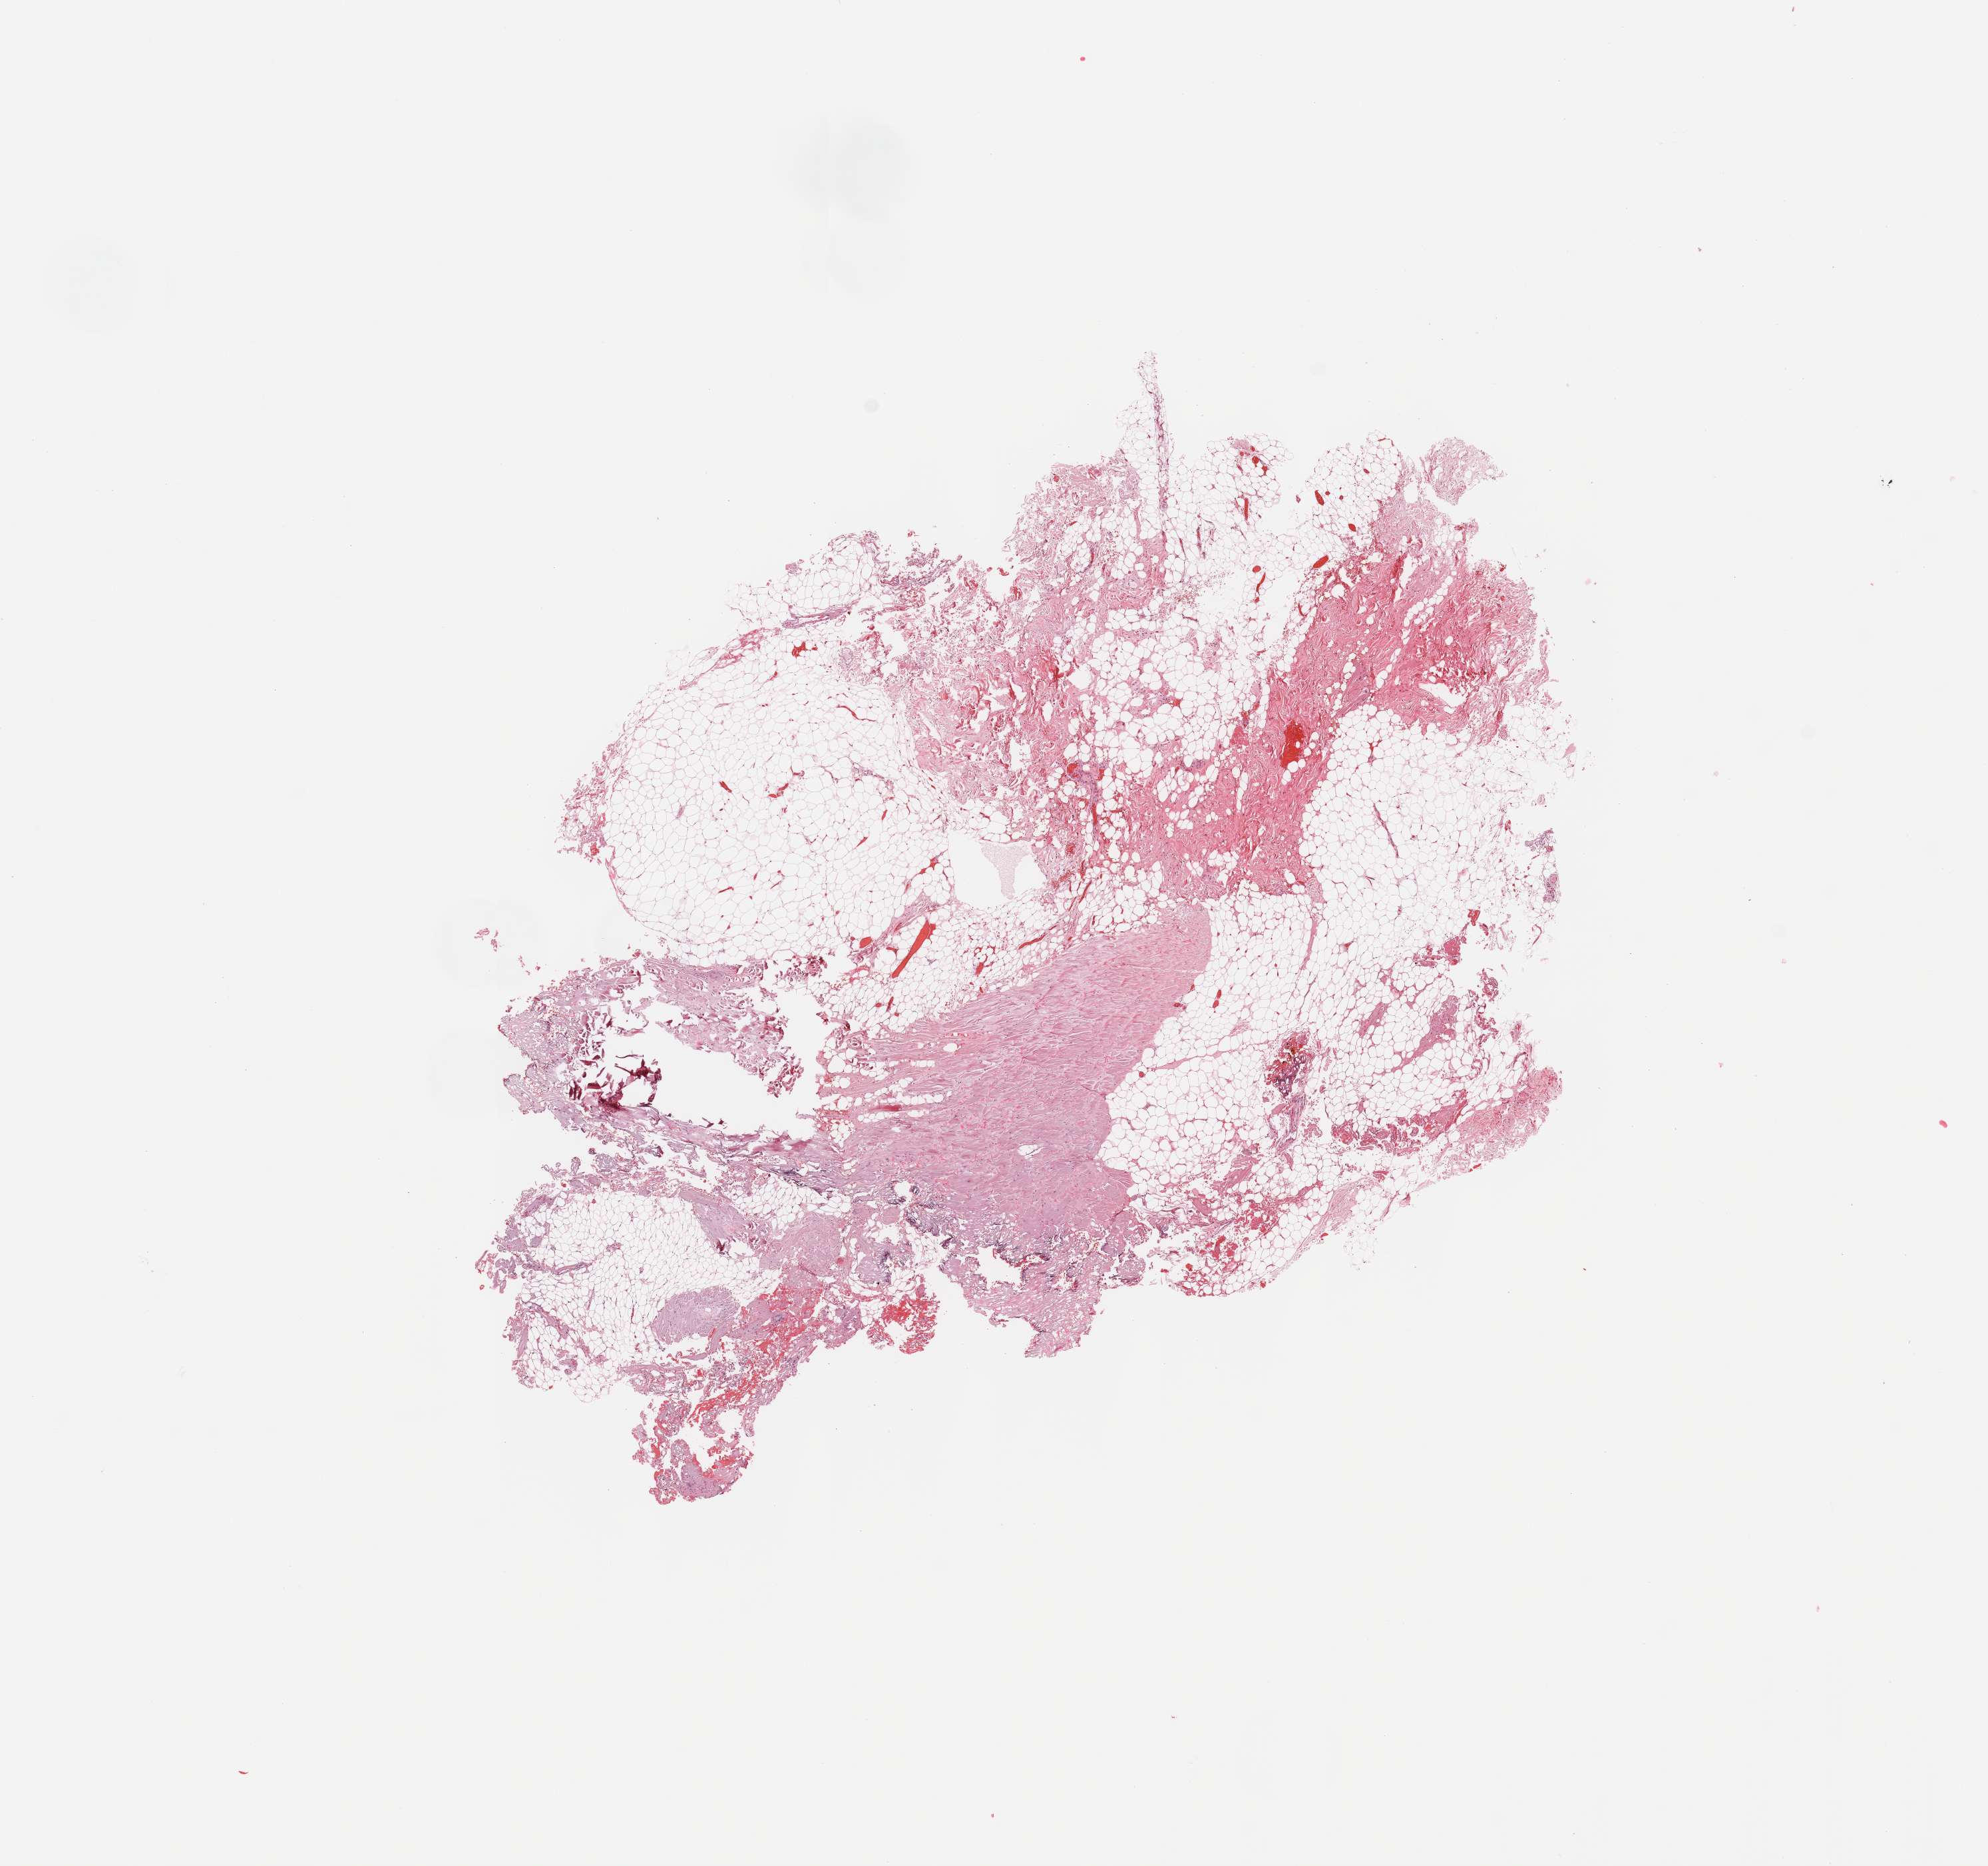
H&E-stained whole-slide image — whole scanned area (about 11.8 x 11.1 mm, slide scanned at 20x) shown as a low-resolution overview. 66-year-old male patient.
Patient diagnosis (cohort enrolment): sarcoma (site not recorded at cohort level). Primary tumour site (as recorded): pelvic.